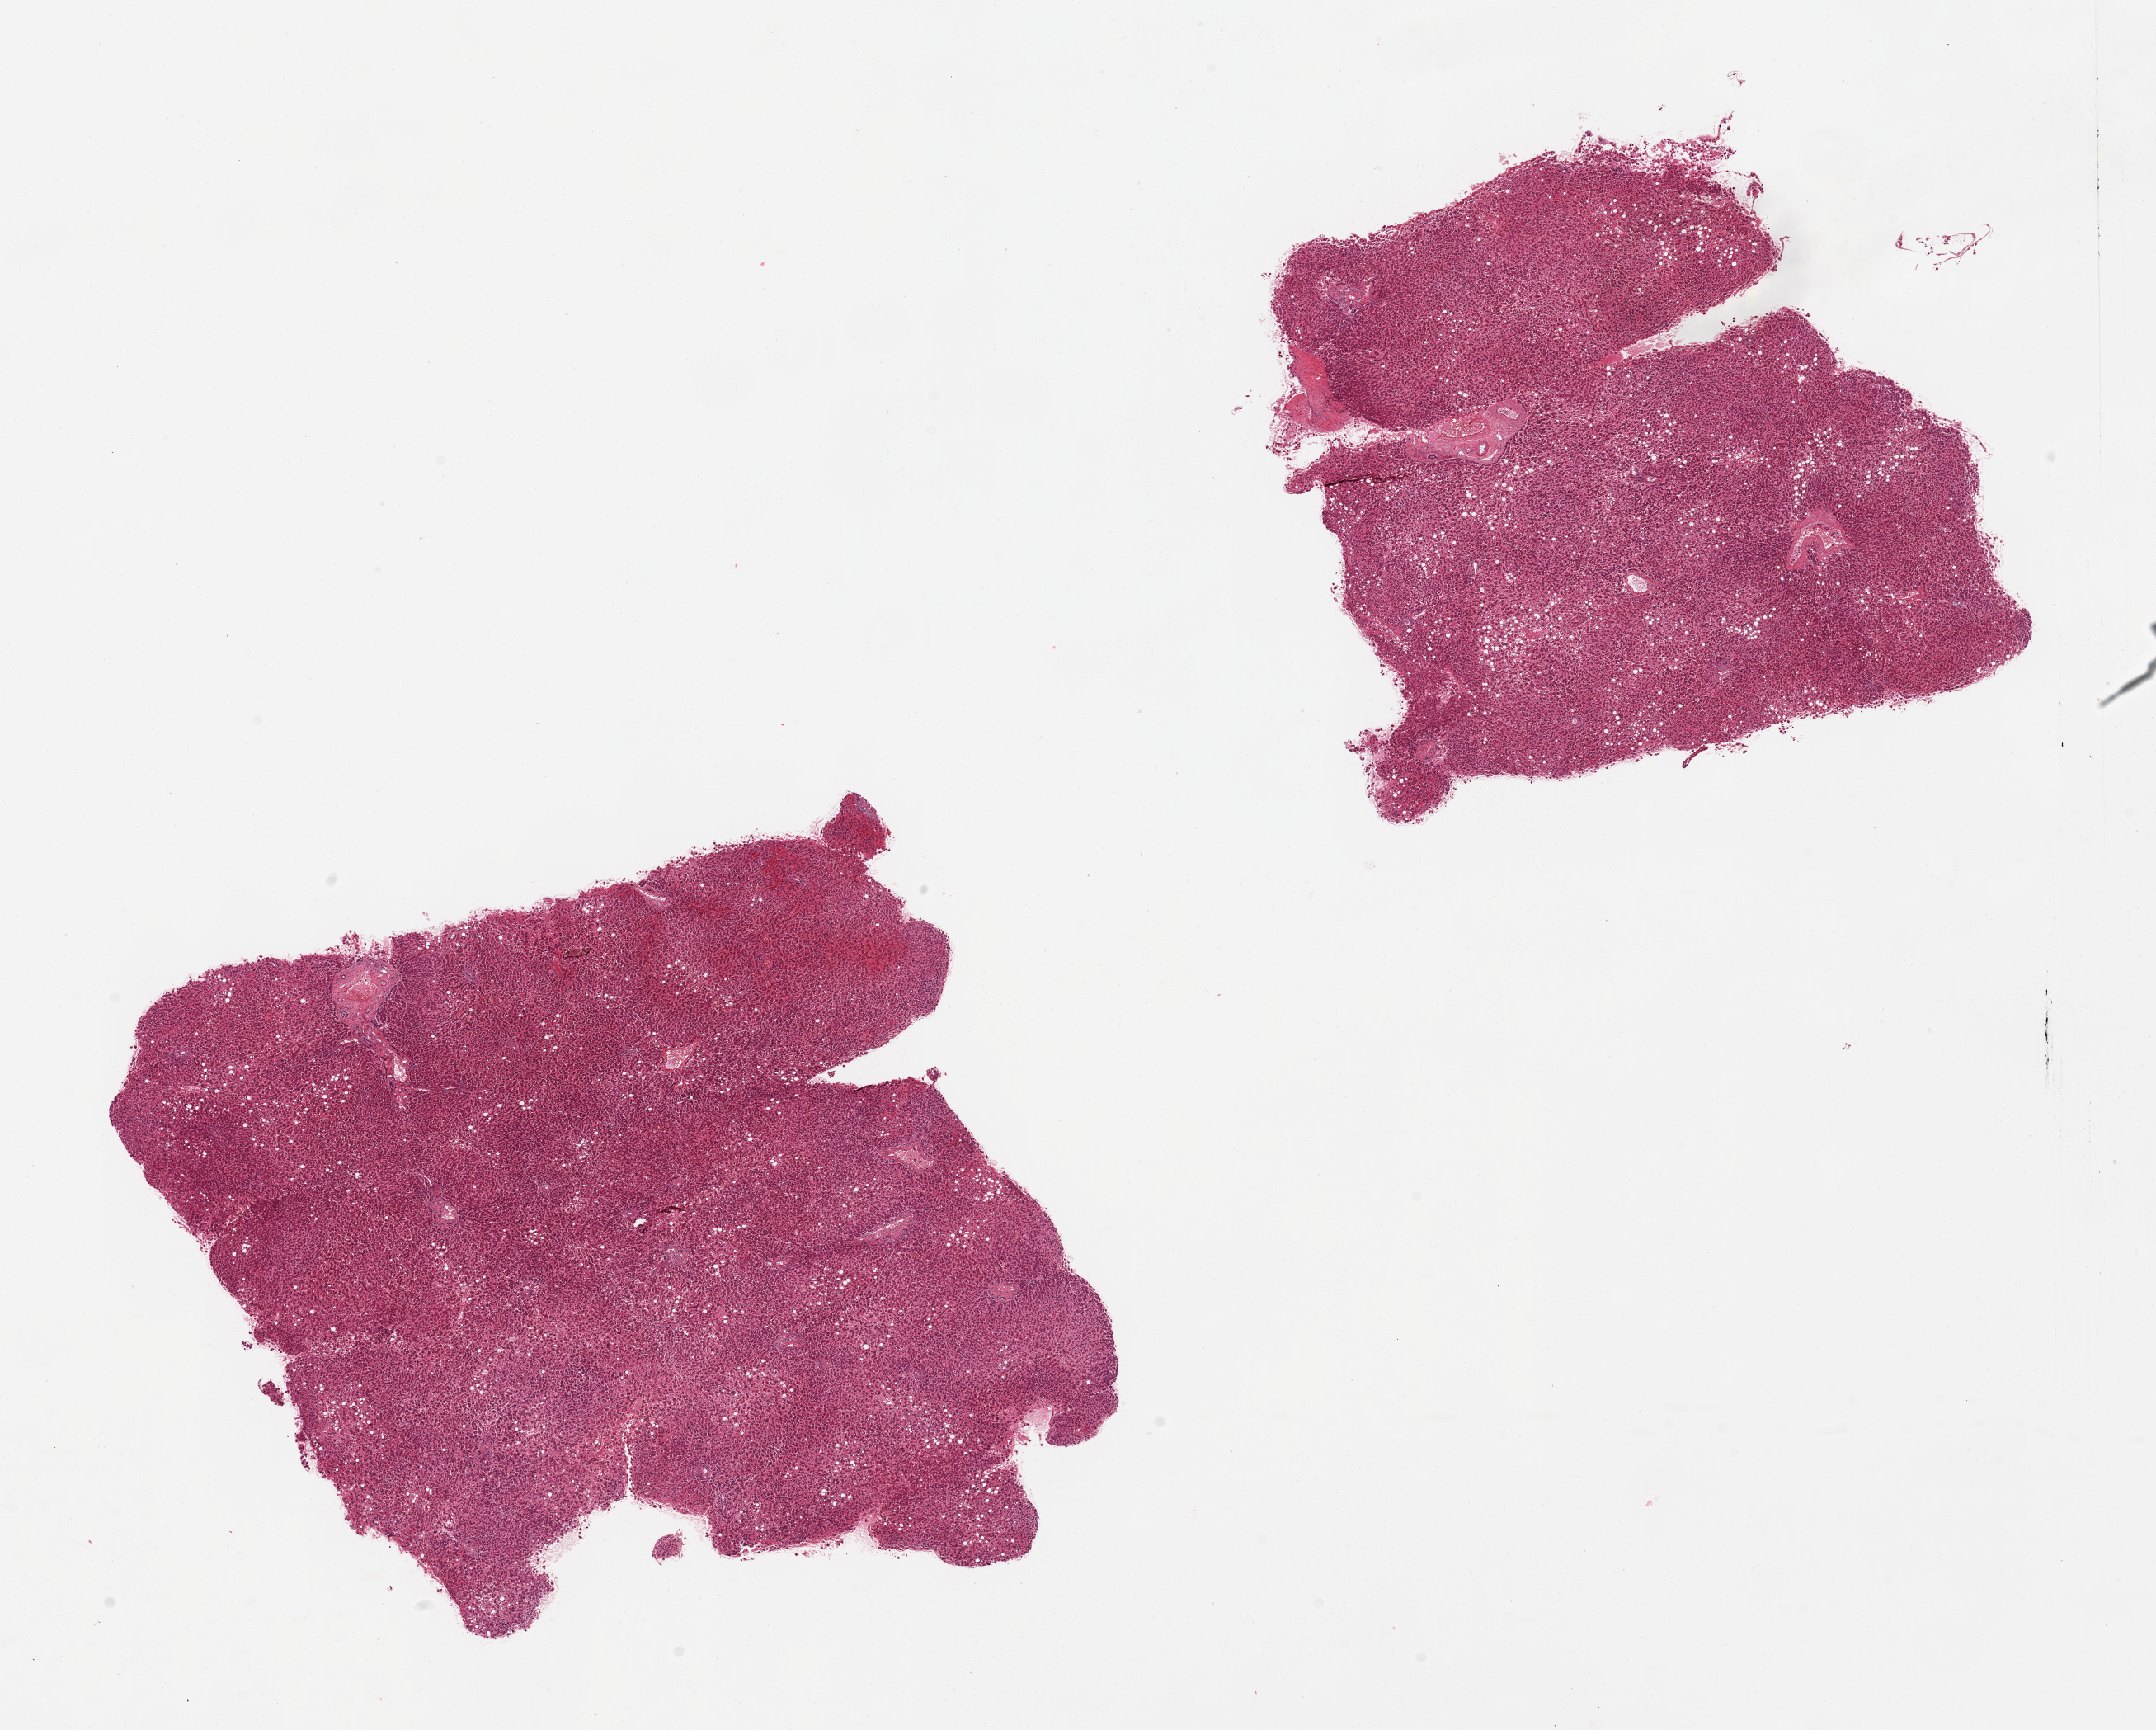
Whole-slide image, haematoxylin and eosin stain — low-resolution overview of the scanned area, about 20.7 x 16.6 mm (slide scanned at 20x). PAXgene-fixed paraffin-embedded (PFPE) section. Sampled site (target tissue): liver. Tissue donor sample. Donor: male.
Review note (as recorded): 2 pieces; congestion and mild fatty change.